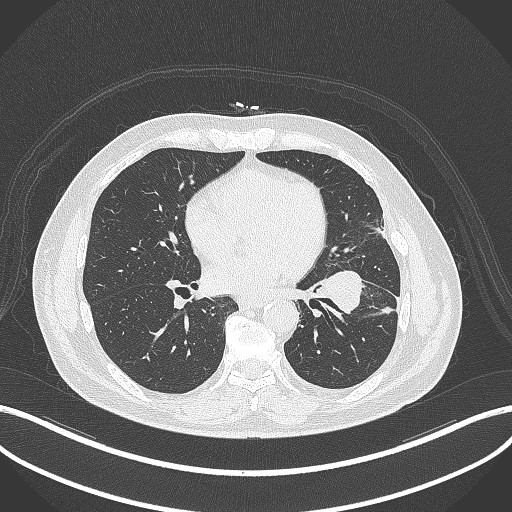
Chest CT, one axial slice; slice 159 of 230 in the series (ordered by position); 120 kVp; lung window (W 1500 / L -600 HU); 512 × 512 image matrix. Male patient, age 68 years. From the clinical record (not read from this slice): clinical TNM (as recorded): T2b N0 M0.
Annotated regions visible in this slice (bounding box drawn by a radiologist):
- lung tumour (recorded histology: squamous cell carcinoma): box from (x=319, y=266) to (x=369, y=319) px